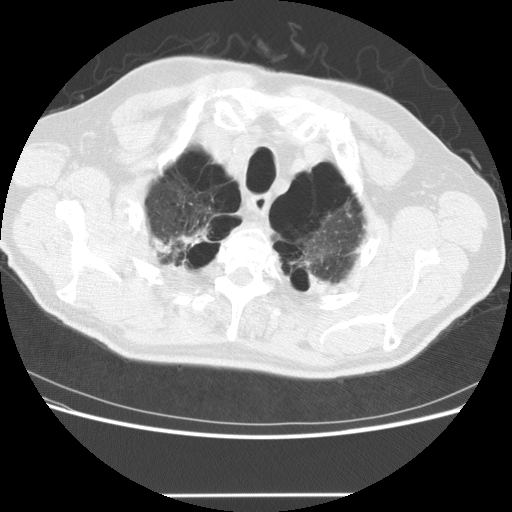
Axial slice from a low-dose chest CT screening exam. Third screening round (two years after baseline). Lung window (W 1500 / L -600 HU). 2.5 mm slice thickness. Slice 25 of 151 in the series. 512 × 512 image matrix. Male, age 68 years at enrolment.
Lesion marked by an expert reader, box from (x=133, y=212) to (x=217, y=282) px. The screening reader recorded 2 non-calcified nodules or masses ≥4 mm on this exam (lingula, left lower lobe); which of them this box marks is not recorded. Official screen result: positive, no significant change: stable abnormalities potentially related to lung cancer, unchanged since the prior screening exam. Participant outcome: lung cancer diagnosed 301 days after this screen — large cell carcinoma, NOS, right upper lobe, poorly differentiated (G3), stage IV (AJCC 6th edition).